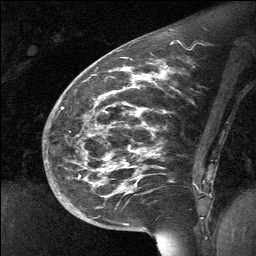
Breast MRI (dynamic contrast-enhanced), one sagittal slice; slice 25 of 64 in the series (ordered by position); dynamic contrast-enhanced study with each time point stored as its own series, time point 2 of 3 at this slice position (early post-contrast, ordered by acquisition time); 1.5 T; TE 4.8 ms, TR 27 ms; 2 mm slice thickness; 256 × 256 image matrix. Patient: female, 39 years. Case-level facts recorded for this patient, not image findings: setting: breast cancer imaged before/during neoadjuvant chemotherapy; receptor status: HER2-positive.
Structures marked on this image (semi-automatically segmented with operator editing):
- analysis volume of interest (the breast-tissue region the enhancement analysis was run in; not a lesion): box from (x=70, y=69) to (x=202, y=224) px
- tumour enhancement mask (voxels above the 90 % enhancement threshold inside the analysis volume of interest): (x=107, y=69)–(x=146, y=95)